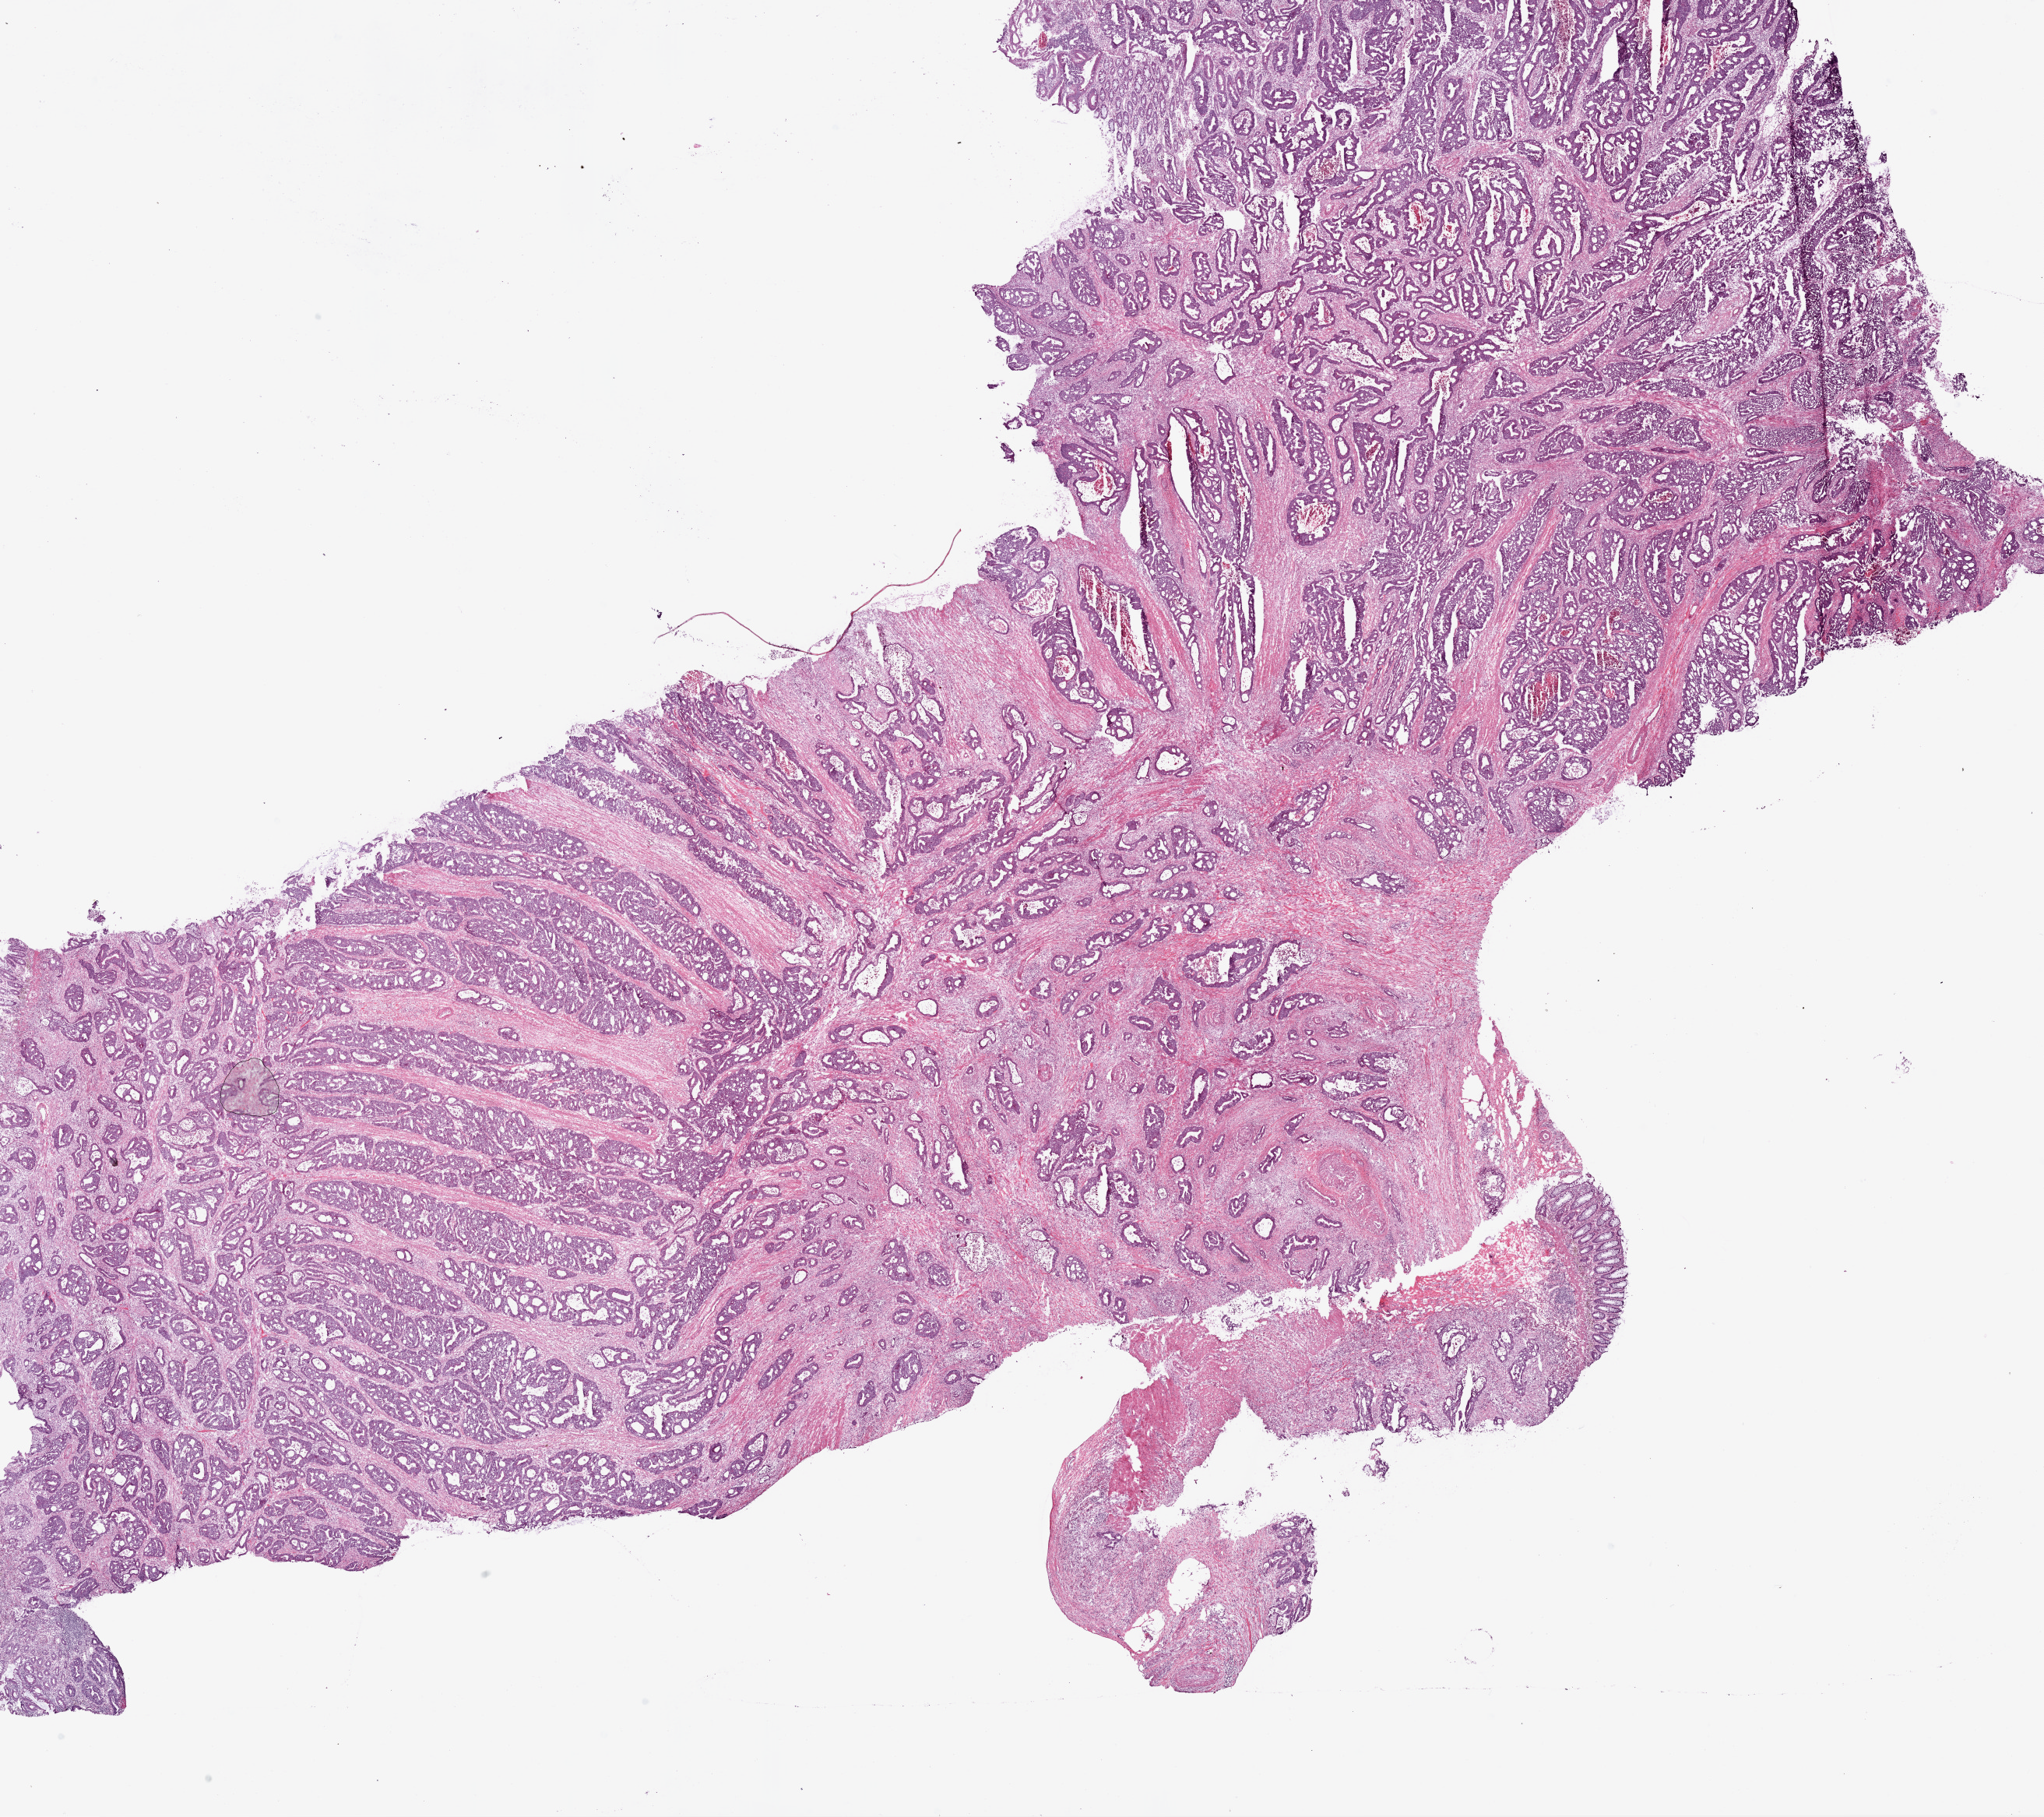
Hematoxylin and eosin (H&E) stained whole-slide image, shown as a low-resolution overview of the whole scanned area (about 21.1 x 18.7 mm), frozen section, primary tumour sample from the colon. Patient: female, age at initial diagnosis 39 years. Slide review estimates, as recorded: tumour cells 95%, tumour nuclei 80%, normal cells 0%, stromal cells 0%, necrosis 5%. Infiltration values recorded for this section: lymphocyte infiltration 5%, monocyte infiltration 1%, neutrophil infiltration 2%.
Lymph nodes positive (case pathology): 3 of 108 examined. AJCC pathologic stage: IIIB (7th edition). TNM: T3 N1b M0. Pathologic diagnosis: Adenocarcinoma, NOS (sigmoid colon).